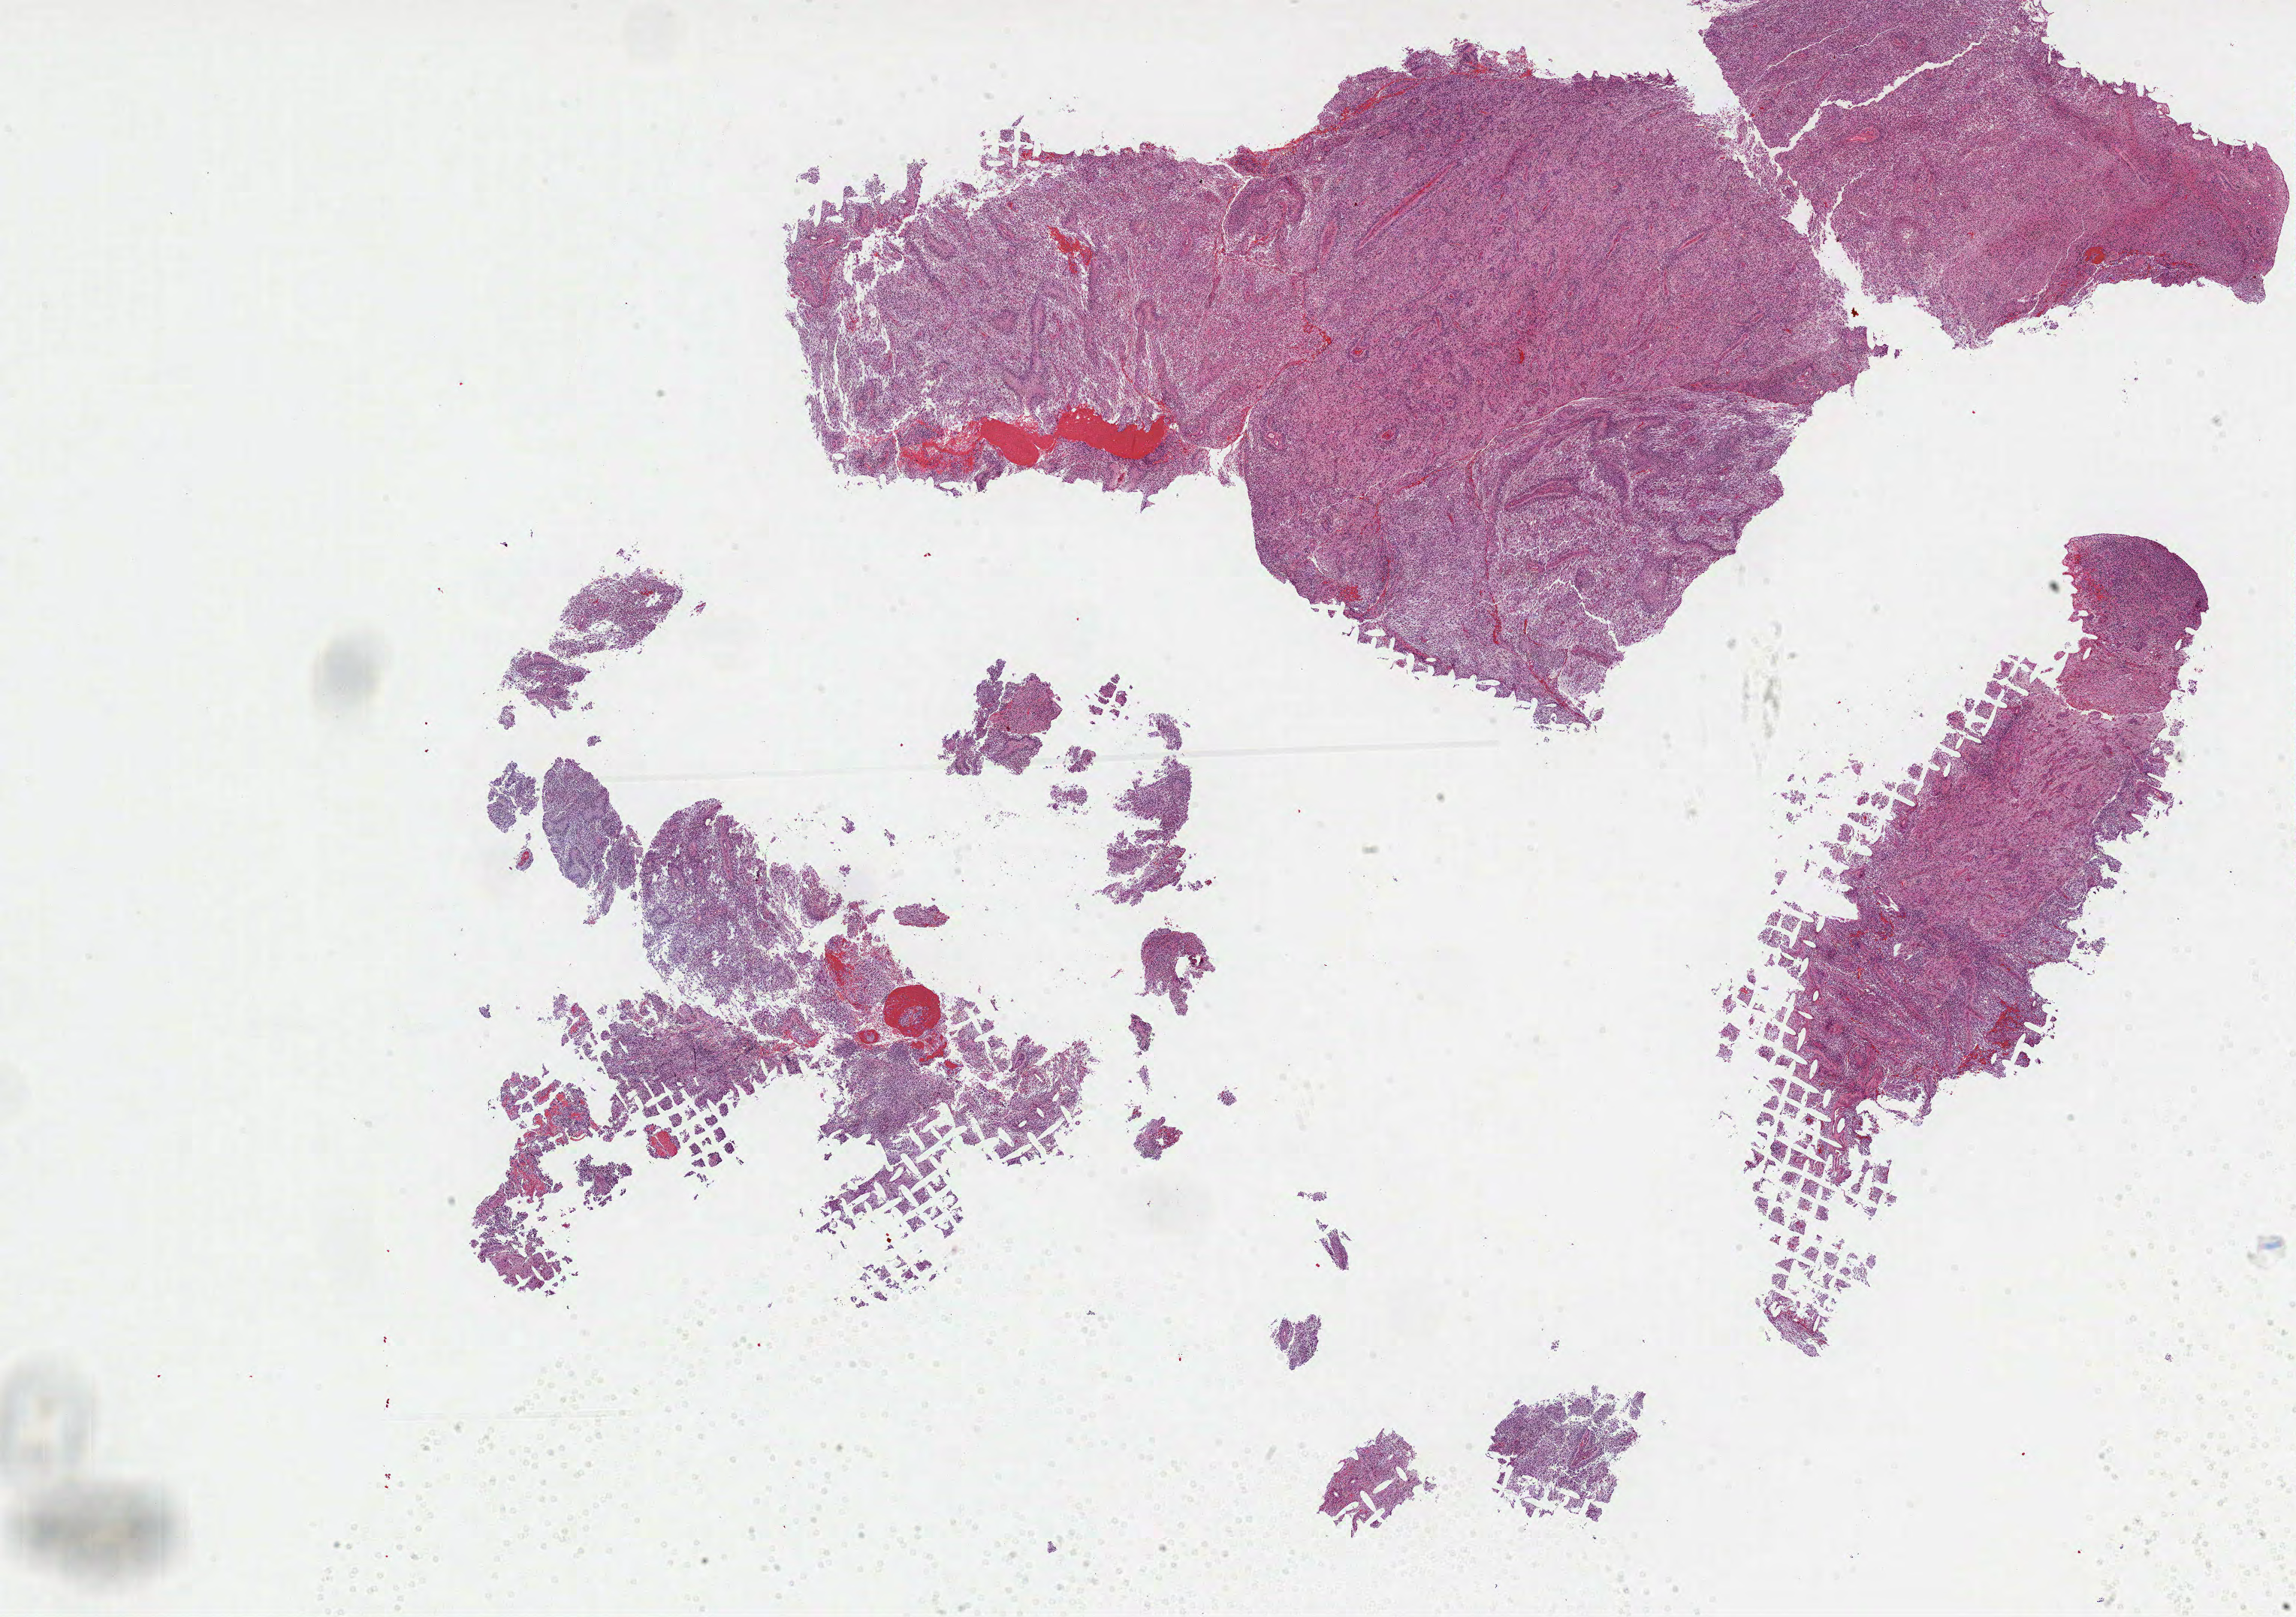
Whole-slide histology image, Hematoxylin and eosin (H&E) stained, shown as a low-resolution overview of the whole scanned area (about 24.7 x 17.4 mm). Formalin-fixed paraffin-embedded (FFPE) diagnostic section. Primary tumour sample from the brain. Male, age 75 years at initial diagnosis.
Pathologic diagnosis: Glioblastoma.